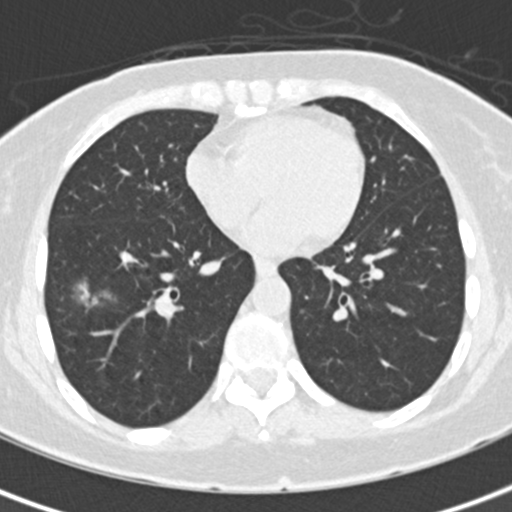
Low-dose screening chest CT, one axial slice; position 70 of 171 along the scan axis; reconstruction kernel B30f; lung window (W 1500 / L -600 HU); 512 × 512 image matrix.
Annotated regions visible in this slice (outlined manually by an expert reader):
- lesion 1 (tumor, lower lobe of right lung): bounding box <73,277,115,307> (left, top, right, bottom; pixels)